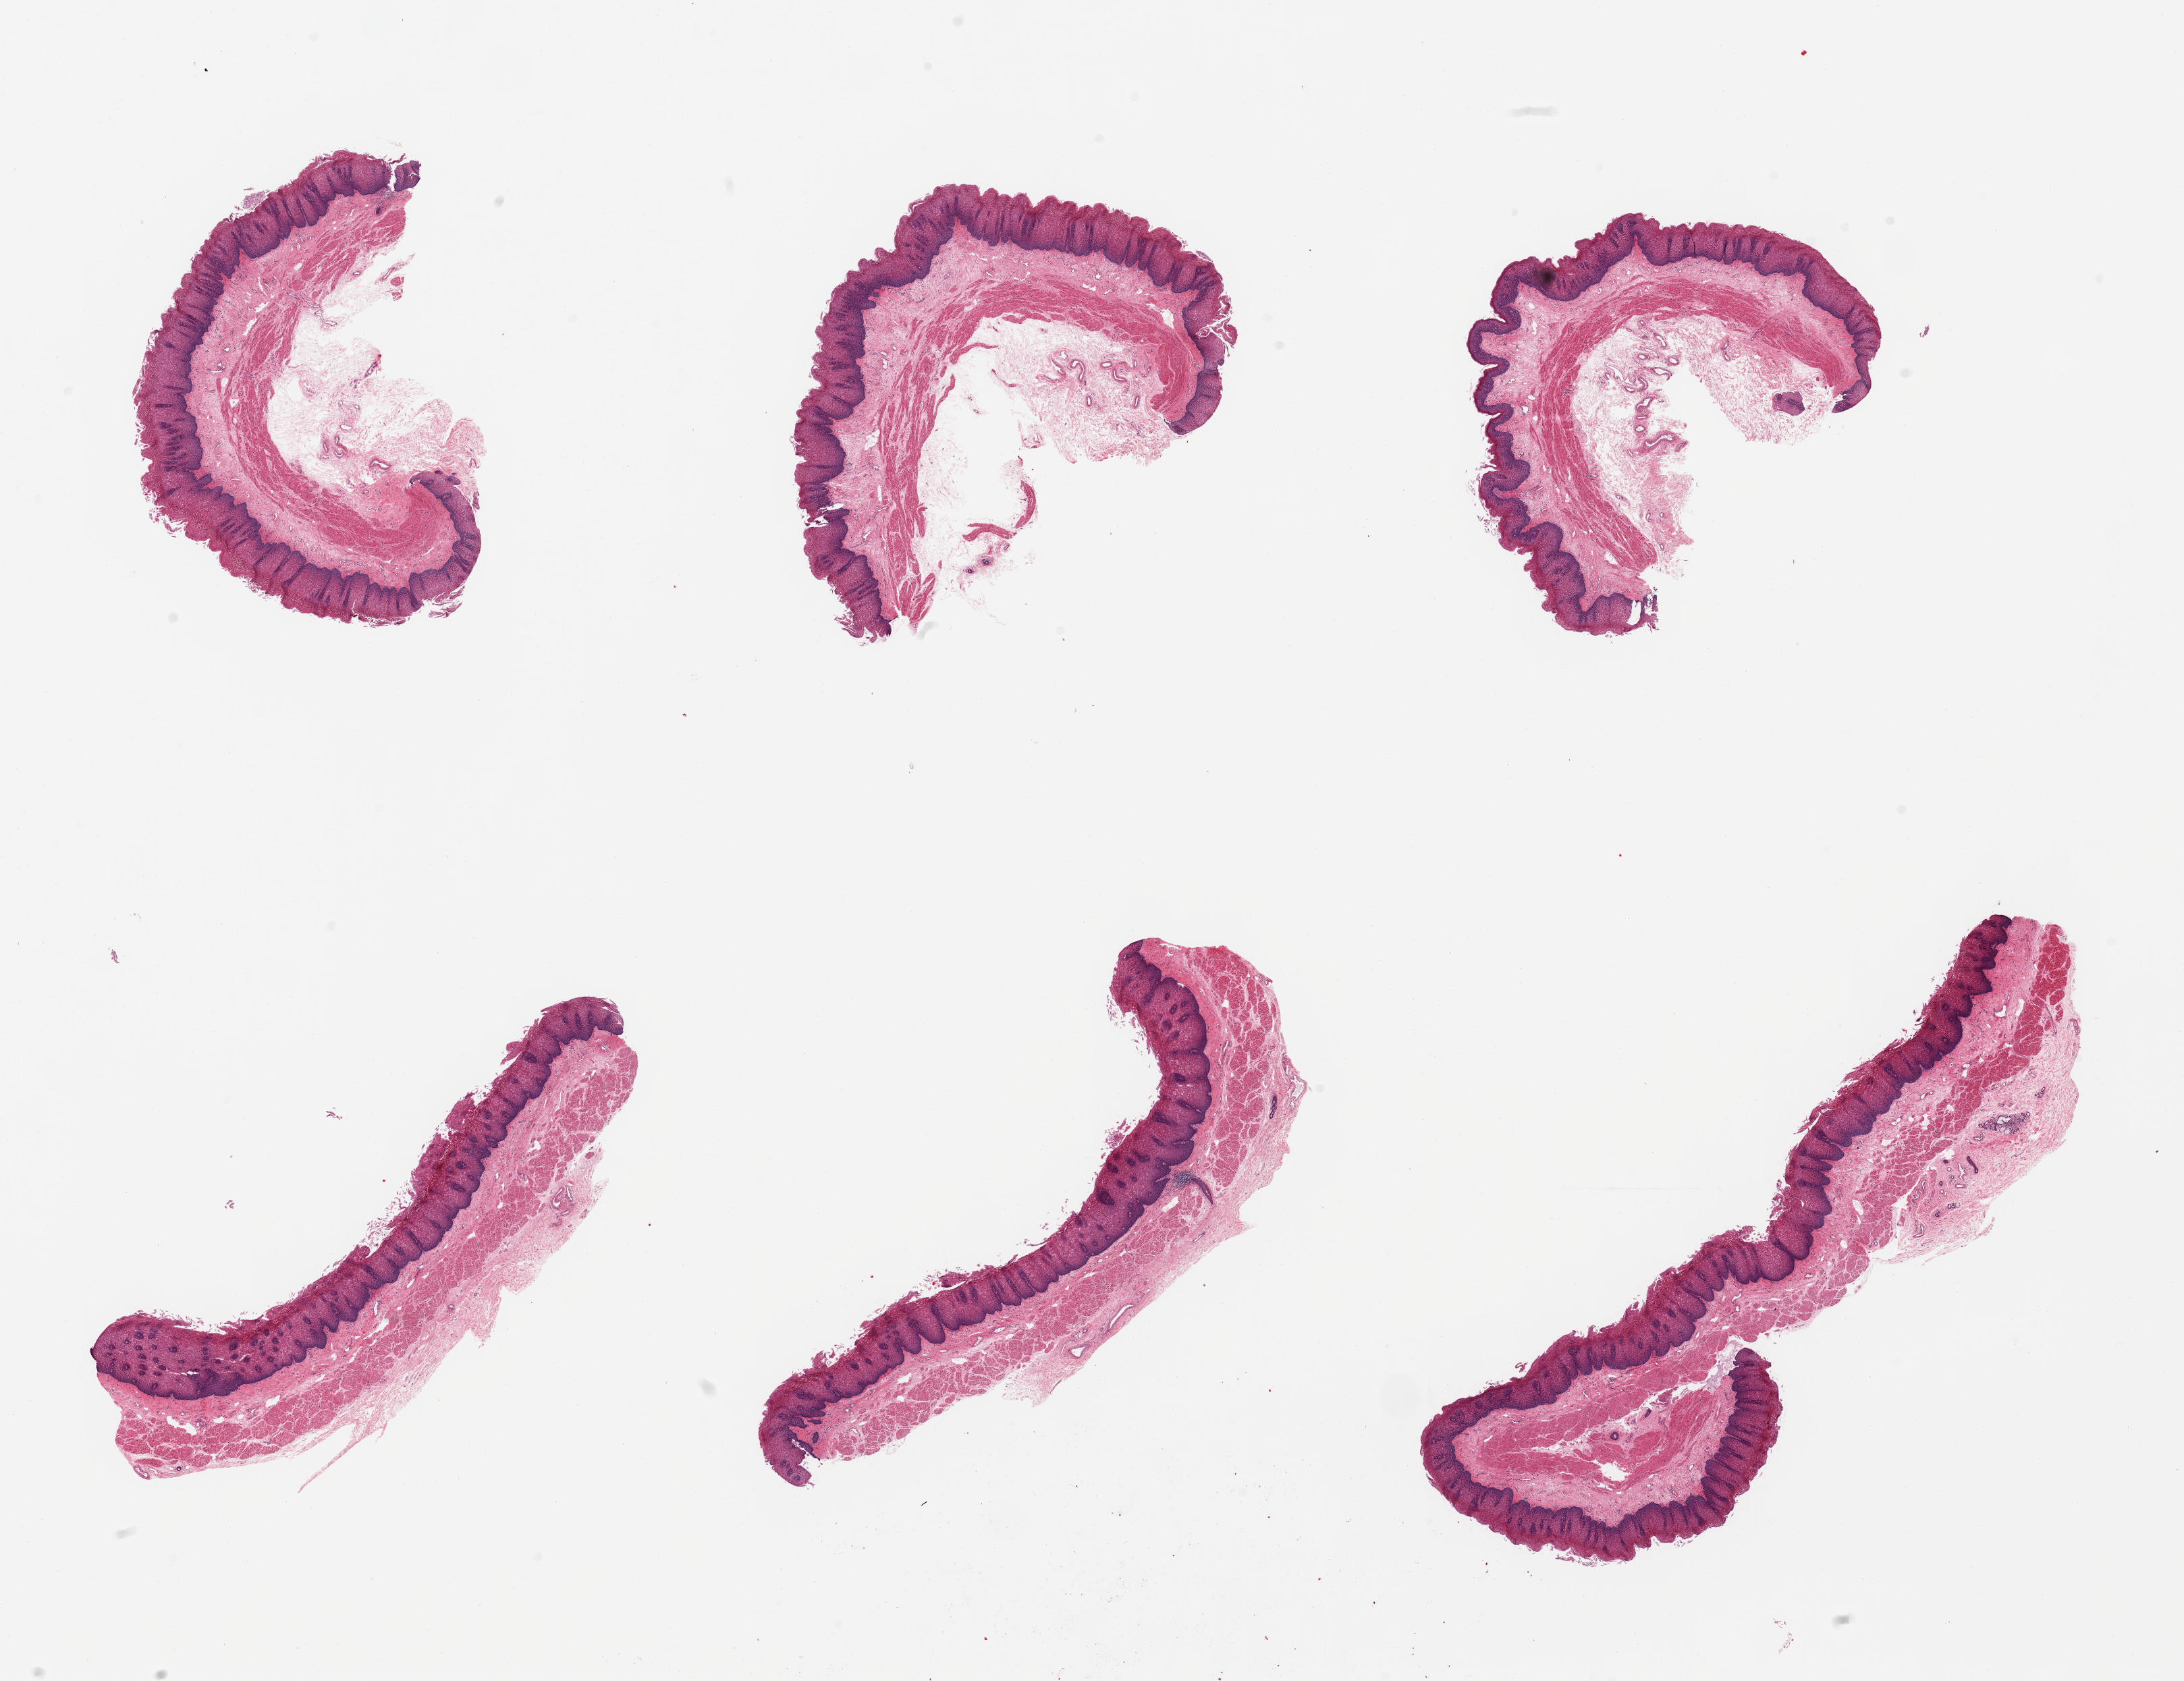
Digitized hematoxylin and eosin (H&E)-stained section — whole scanned area (about 25.6 x 19.7 mm, slide scanned at 20x) shown as a low-resolution overview; PAXgene-fixed paraffin-embedded (PFPE) section; sampled site (target tissue): esophageal mucous membrane; tissue donor sample.
* reviewer comment on this tissue sample: 6 pieces, squamous mucosa is ~0.5mm ~25% thickness